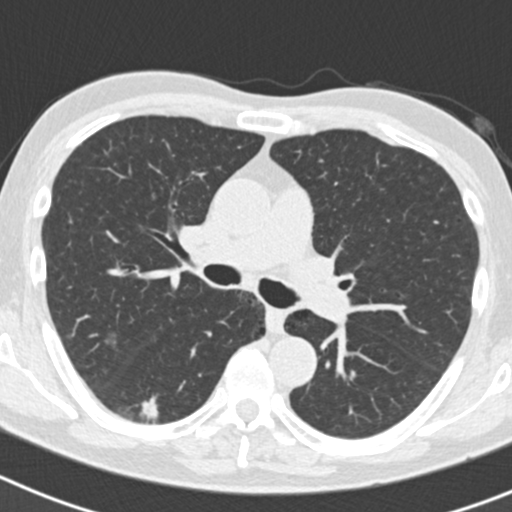
Axial slice from a low-dose chest CT screening exam. Second screening round (one year after baseline). Lung window (W 1500 / L -600 HU). 2 mm slice thickness. 120 kVp. Male participant, aged 70 years at enrolment.
Expert-annotated lung lesion, bounding box <135,382,193,435> (left, top, right, bottom; pixels). The screening reader recorded 5 non-calcified nodules or masses ≥4 mm on this exam (right lower lobe, right lower lobe, right upper lobe, right upper lobe, left upper lobe); which of them this box marks is not recorded. Official screen result: positive, other.